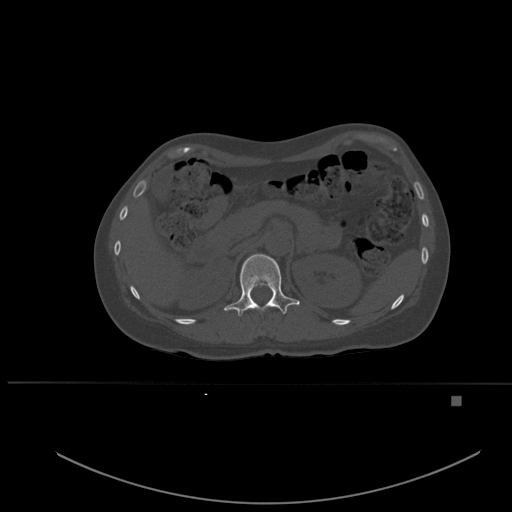
CT including the spine, one axial slice. Position 255 of 651 along the scan axis. Bone window (W 1800 / L 400 HU). 1.5 mm slice thickness. 512 × 512 image matrix, field of view 443 × 443 mm. Female patient, age 49 years. From the clinical record (not read from this slice): primary cancer: breast; vertebrae with lytic lesions (as recorded): L3, T12, L4.
Outlined on this slice (semi-automatic segmentation, software-assisted and operator-edited):
- T12 vertebra: bounding box (x1, y1, x2, y2) in pixels: (224, 254, 300, 316)